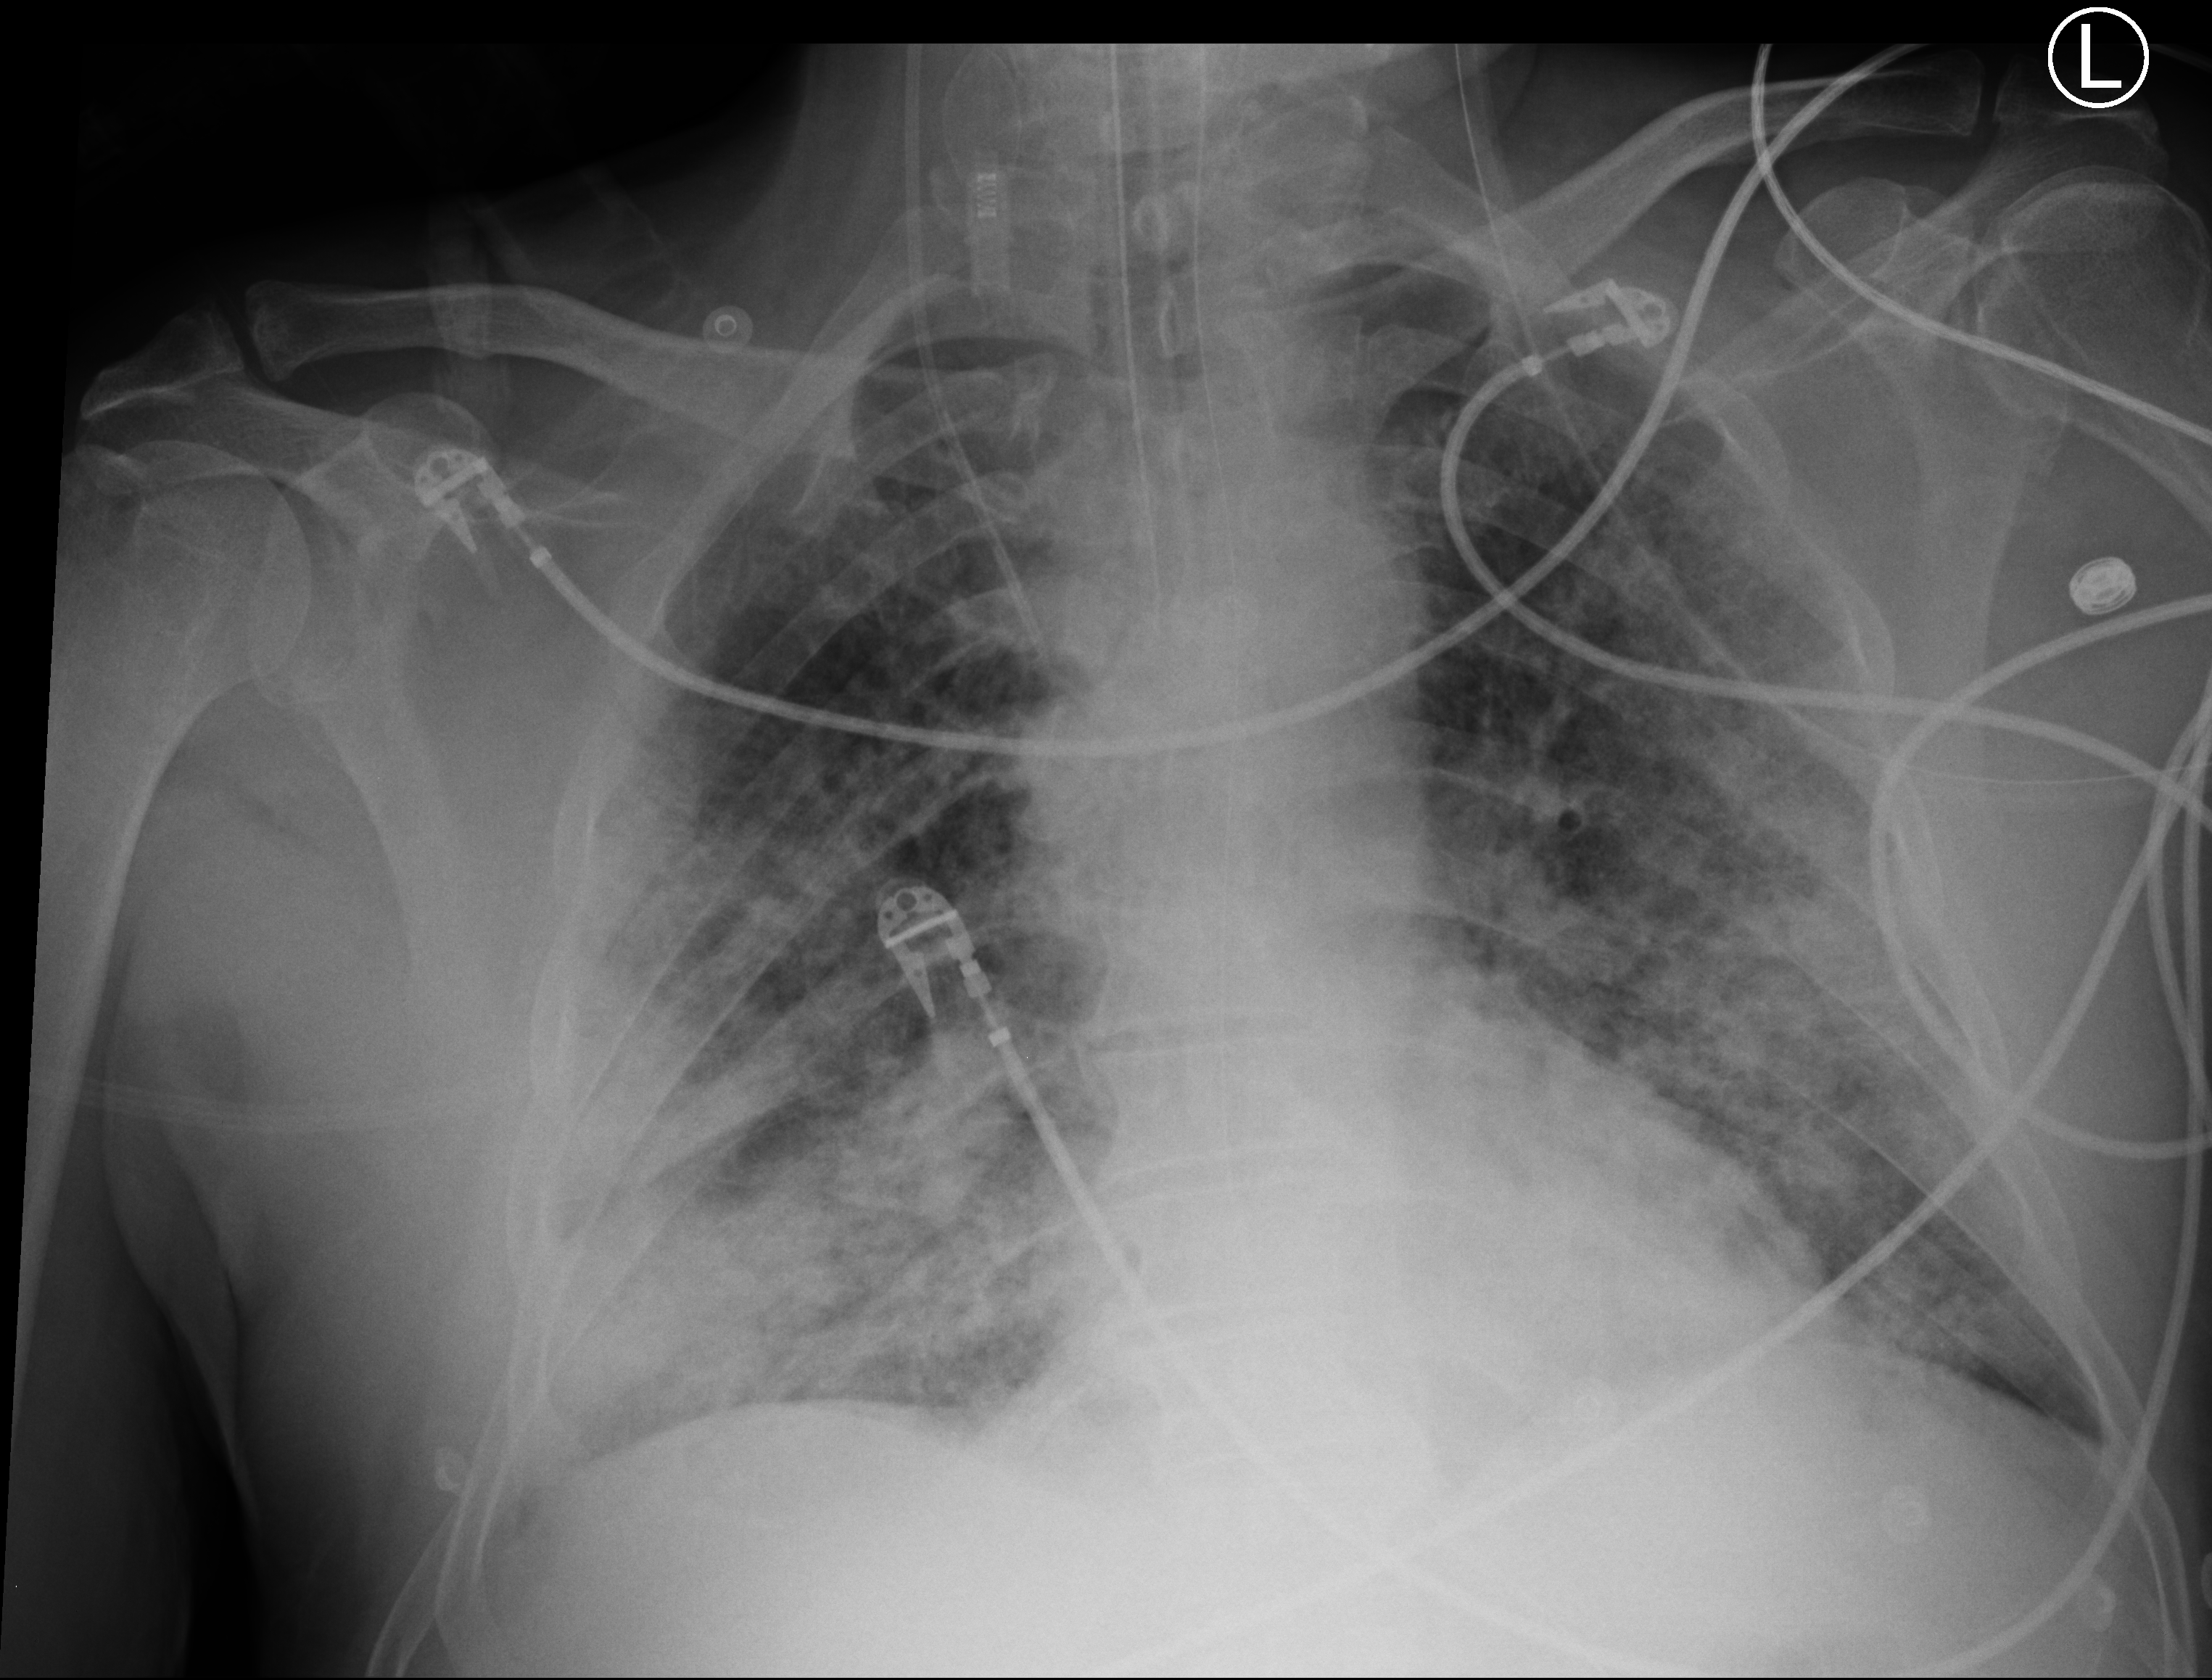
Portable chest radiograph; anteroposterior (AP) projection. Male patient hospitalised with COVID-19, age 60–74 years.
Admission-level facts for this patient (not findings on this image; timing relative to this image not recorded):
- smoking status (admission record): never
- admitted to intensive care during this hospital stay: yes
- mechanically ventilated during this hospital stay: yes